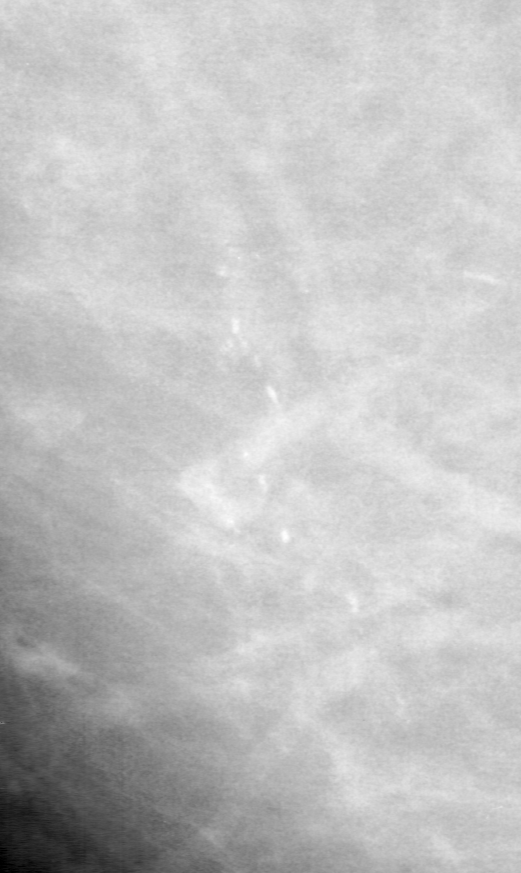
Region of interest cut from a scanned film mammogram (one marked finding), left breast, CC view, BI-RADS breast density category 2 (scale 1–4).
Marked abnormality: calcifications, morphology pleomorphic, distribution linear; BI-RADS assessment category 4; subtlety rating 4 on a 1 (subtle) to 5 (obvious) scale; pathology (as recorded): malignant.